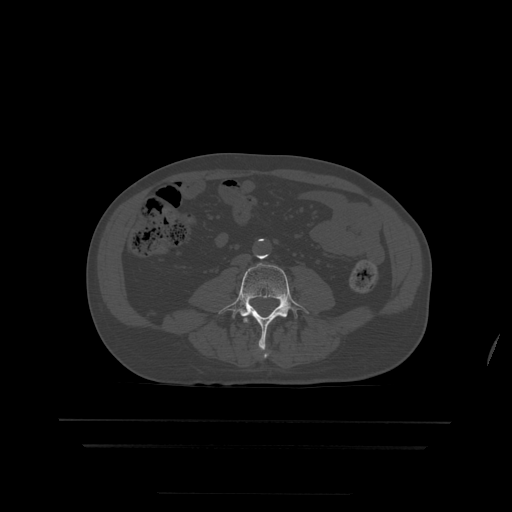
CT including the spine, one axial slice. Bone window (W 1800 / L 400 HU). 1.25 mm slice thickness. 512 × 512 image matrix, field of view 436 × 436 mm. Patient age 68 years. Case-level facts recorded for this patient, not image findings: primary cancer: urothelial.
Annotated regions visible in this slice (semi-automatically segmented with operator editing):
- L3 vertebra: bounding box (x1, y1, x2, y2) in pixels: (244, 318, 250, 323)
- L4 vertebra: (219, 263, 309, 357)